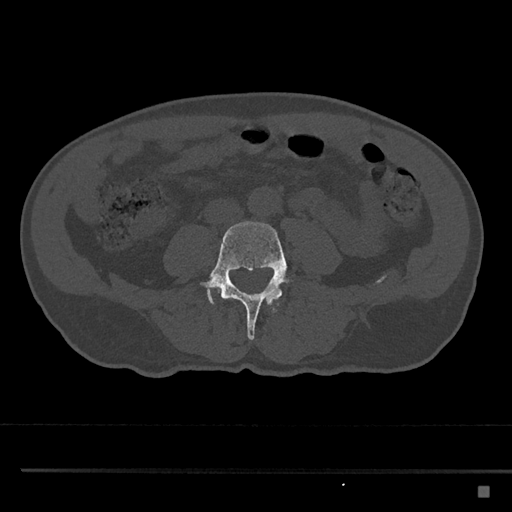
CT including the spine, one axial slice. Slice 636 of 797 in the series (ordered by position). Reconstruction kernel Br40s/3. Bone window (W 1800 / L 400 HU). 0.5 mm slice thickness. 512 × 512 image matrix, field of view 391 × 391 mm. Patient: male, 59 years. Case-level facts recorded for this patient, not image findings: primary cancer: prostate.
Outlined on this slice (semi-automatically segmented with operator editing):
- L3 vertebra: bounding box (x1, y1, x2, y2) in pixels: (224, 296, 281, 313)
- L4 vertebra: (200, 221, 289, 341)
- L5 vertebra: (206, 276, 217, 305)